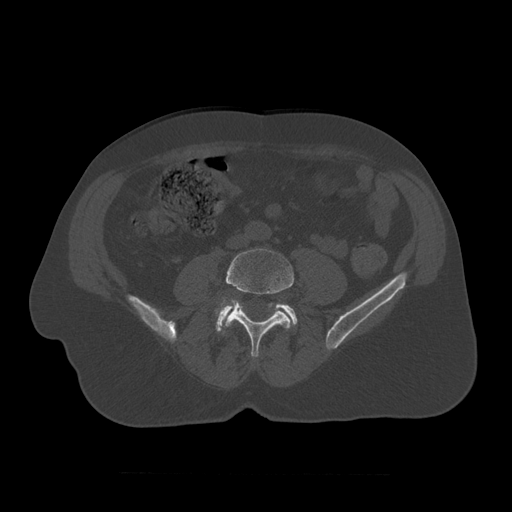
CT including the spine, one axial slice. Position 272 of 450 along the scan axis. 120 kVp. Bone window (W 1800 / L 400 HU). 1.25 mm slice thickness. 512 × 512 image matrix, field of view 405 × 405 mm. Patient age 75 years. From the clinical record (not read from this slice): primary cancer: prostate.
Annotated regions visible in this slice (semi-automatically segmented with operator editing):
- L4 vertebra: bounding box (x1, y1, x2, y2) in pixels: (215, 249, 294, 358)
- L5 vertebra: (216, 302, 298, 334)